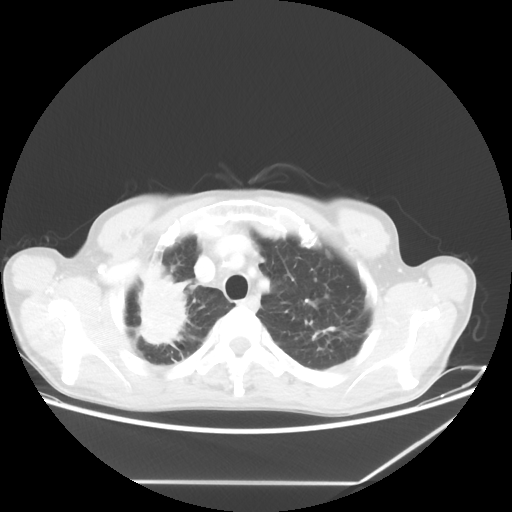
Chest CT, one axial slice. Slice 54 of 65 in the series (ordered by position). Reconstruction kernel STANDARD. 80 kVp. Lung window (W 1500 / L -600 HU). 5 mm slice thickness. 512 × 512 image matrix, field of view 397 × 397 mm. Patient: male, 68 years. From the clinical record (not read from this slice): clinical TNM (as recorded): T3 N3 M0.
Structures marked on this image (bounding box drawn by a radiologist):
- lung tumour (recorded histology: adenocarcinoma): bounding box (x1, y1, x2, y2) in pixels: (122, 255, 207, 377)